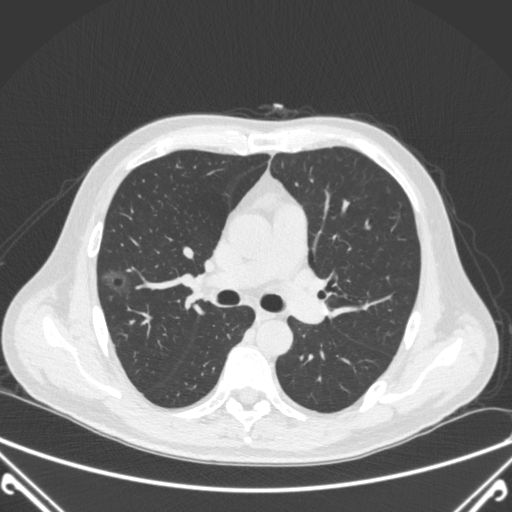
Chest CT, one axial slice; position 225 of 360 along the scan axis; 120 kVp; lung window (W 1500 / L -600 HU); 1 mm slice thickness; 512 × 512 image matrix, field of view 380 × 380 mm. Male patient, age 64 years. From the clinical record (not read from this slice): clinical TNM (as recorded): T1c N0 M0; histopathological grade: G2.
Outlined on this slice (bounding box drawn by a radiologist):
- lung tumour (recorded histology: adenocarcinoma): bounding box (x1, y1, x2, y2) in pixels: (102, 257, 133, 304)